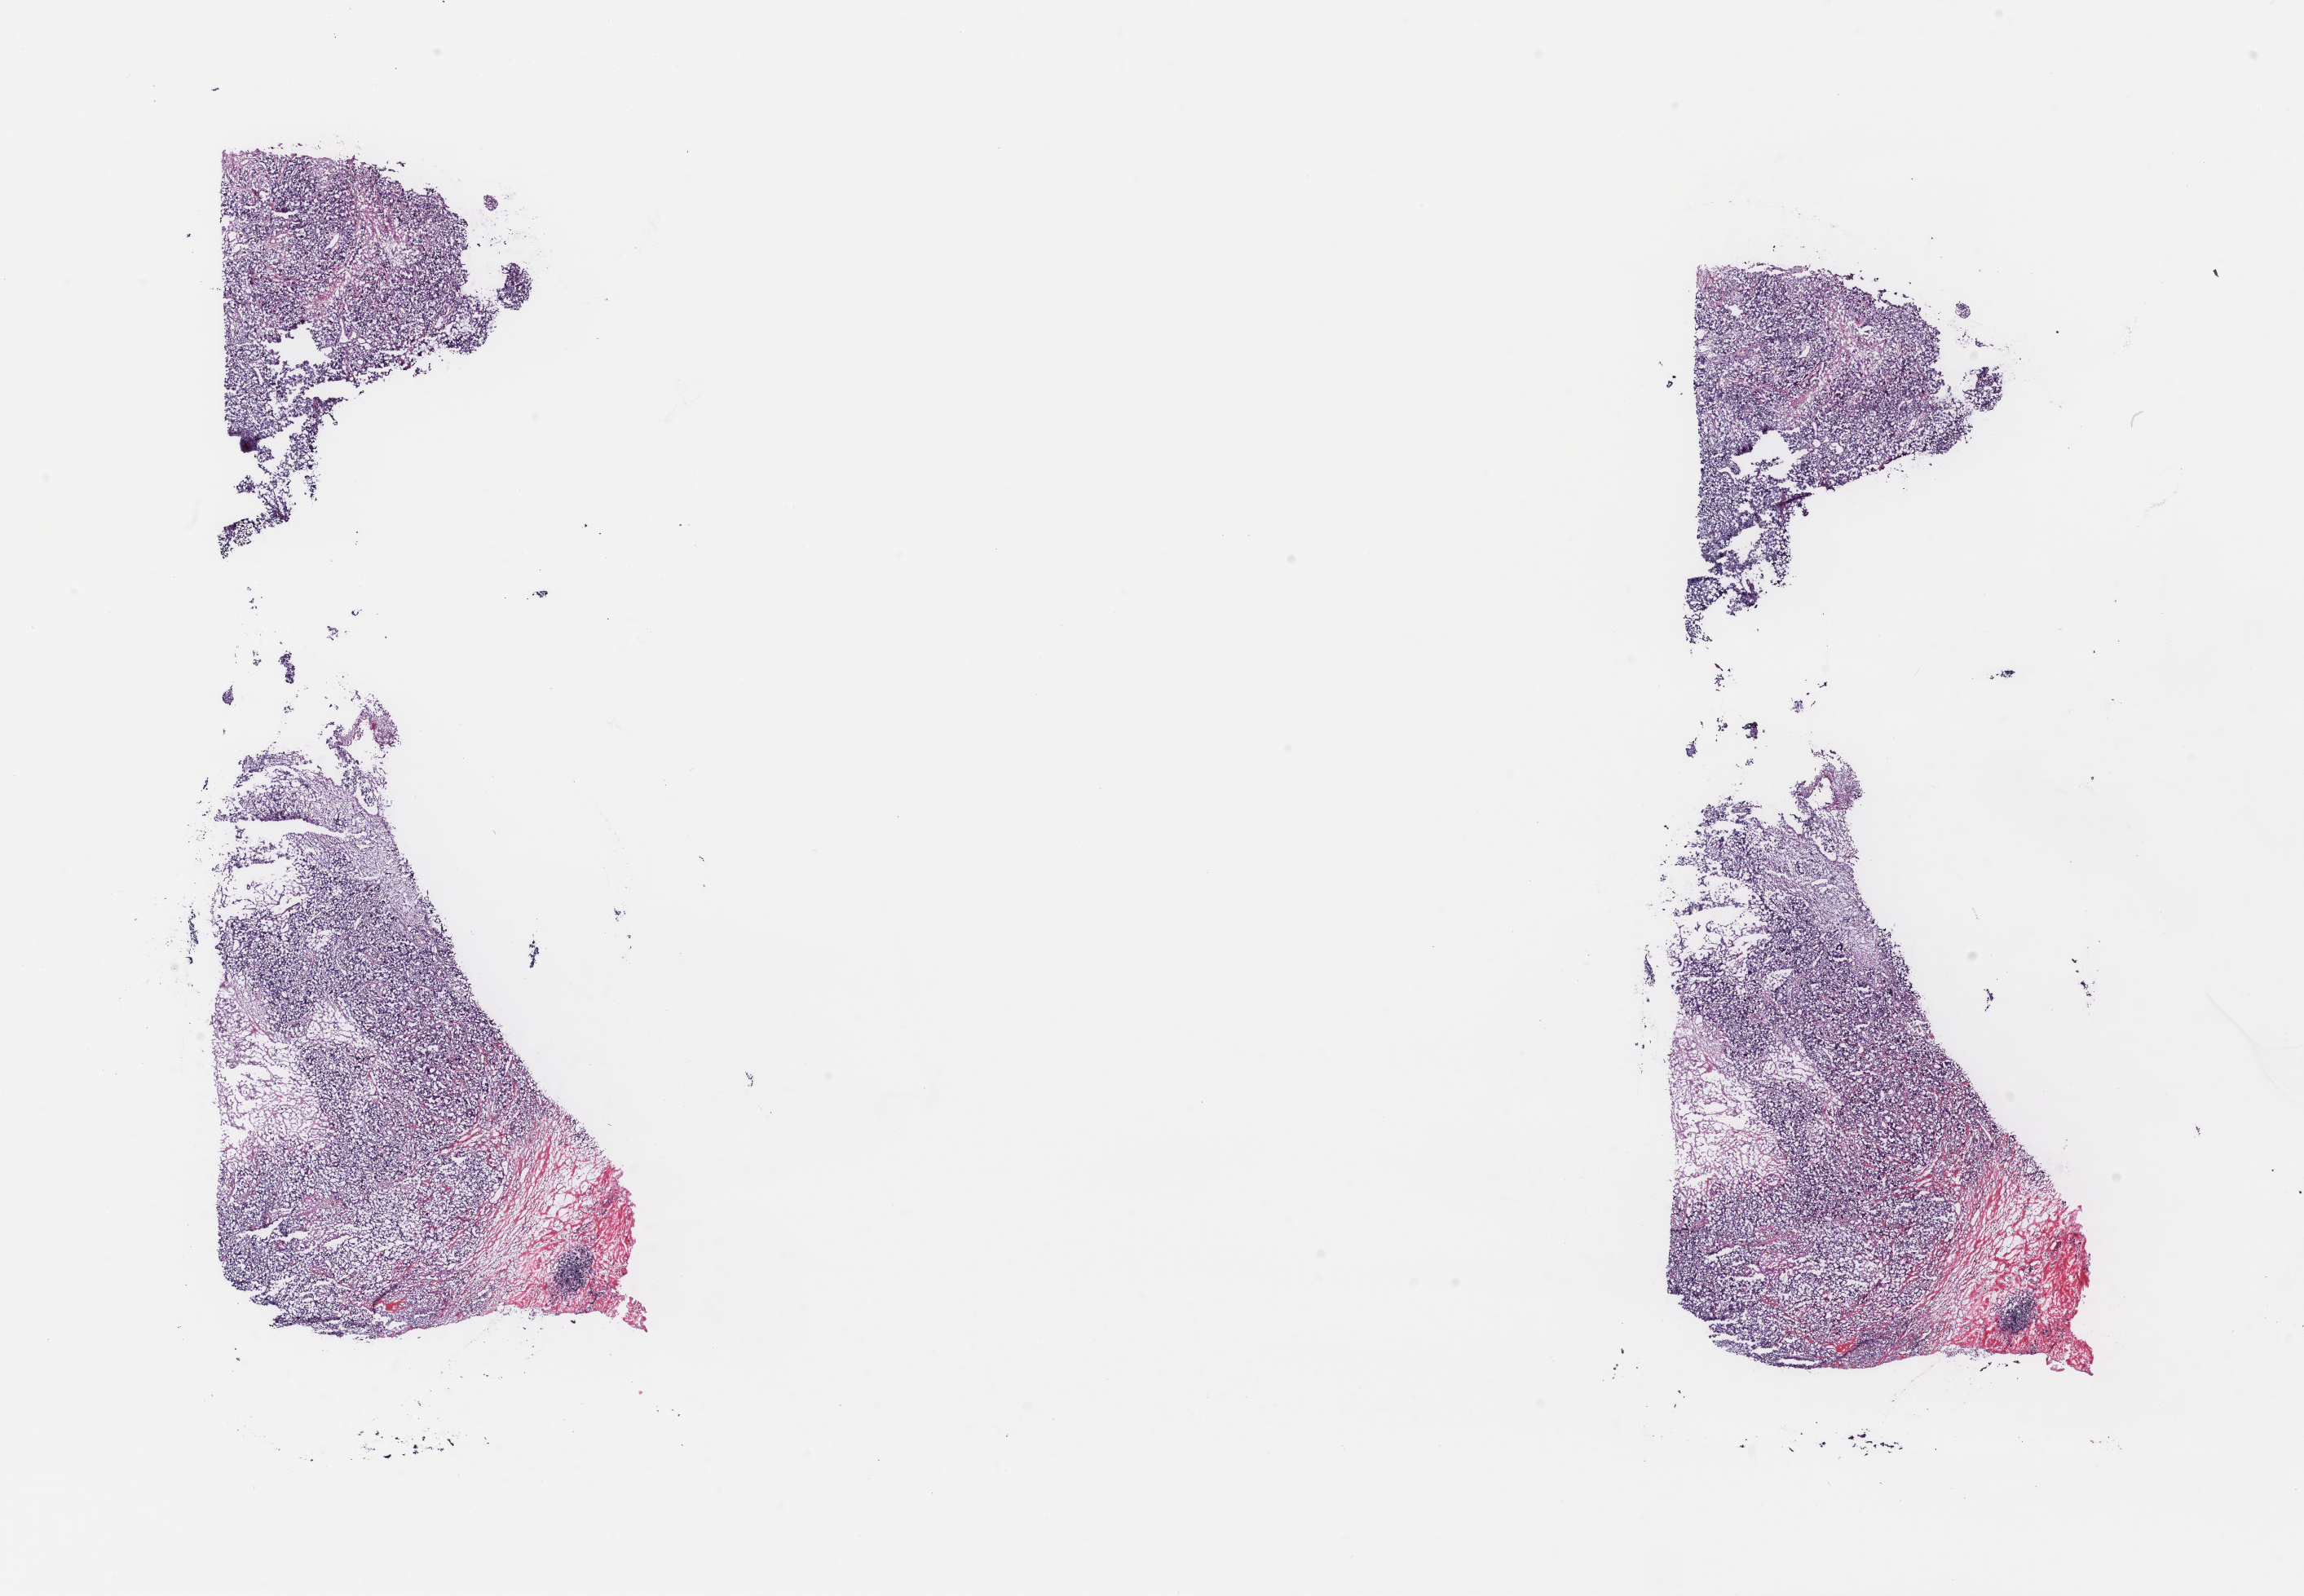
Whole-slide histology image, H&E-stained, shown as a low-resolution overview of the whole scanned area (about 22.4 x 15.5 mm). Frozen section from the top of the tissue portion. Sample: primary tumour, breast. Patient: female, age at initial diagnosis 29 years. Pathologist review of this section (percent, as recorded): tumour cells 85%, tumour nuclei 75%, normal cells 0%, stromal cells 0%, necrosis 15%. Inflammatory infiltration, as recorded: lymphocyte infiltration 0%, monocyte infiltration 0%, neutrophil infiltration 0%.
* lymph nodes positive (case pathology): 2 of 21 examined
* TNM: T2 N1a M0
* AJCC pathologic stage: IIB
* laterality: left
* pathologic diagnosis: Infiltrating duct carcinoma, NOS